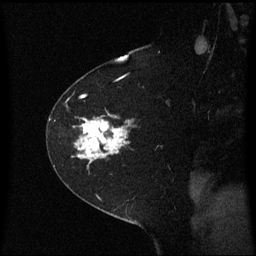
Breast MRI (dynamic contrast-enhanced), one sagittal slice. Position 45 of 60 along the scan axis. Dynamic contrast-enhanced series, image 2 of 3 at this slice position (ordered by acquisition). 1.5 T. TE 4.2 ms, TR 8.4 ms. 2 mm slice thickness. 256 × 256 image matrix. Female patient, age 60 years. From the clinical record (not read from this slice): setting: breast cancer imaged before/during neoadjuvant chemotherapy; receptor status: triple-negative.
Structures marked on this image (semi-automatically segmented with operator editing):
- analysis volume of interest (the breast-tissue region the enhancement analysis was run in; not a lesion): bounding box [x1, y1, x2, y2] px = [48, 99, 137, 181]
- tumour enhancement mask (voxels above the 70 % enhancement threshold inside the analysis volume of interest): [77, 119, 129, 160]